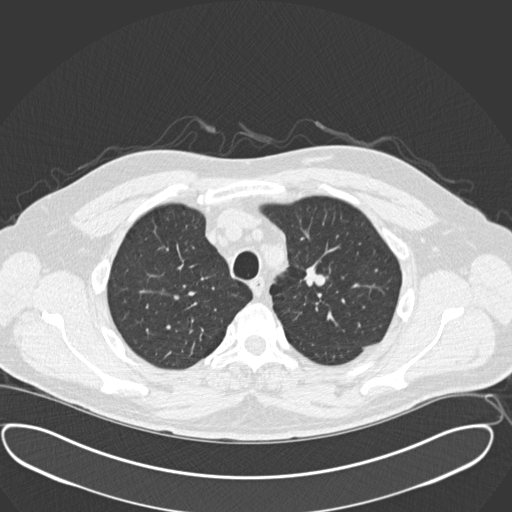
Axial slice from a low-dose chest CT screening exam. Third annual screen. Lung window (W 1500 / L -600 HU). 2 mm slice thickness. Standard (soft-tissue) reconstruction kernel (B30f). 512 × 512 image matrix, field of view 416 × 416 mm. Male participant, aged 56 years at enrolment. Current smoker at enrolment.
Expert-annotated lung lesion, bounding box (x1, y1, x2, y2) in pixels: (290, 261, 342, 308). Screening reader's record for this exam: no non-calcified nodule ≥4 mm recorded. Participant outcome: lung cancer diagnosed 156 days after this screen — neuroendocrine carcinoma, NOS, left upper lobe, well differentiated (G1), stage IA (AJCC 6th edition), 20 mm at pathology.